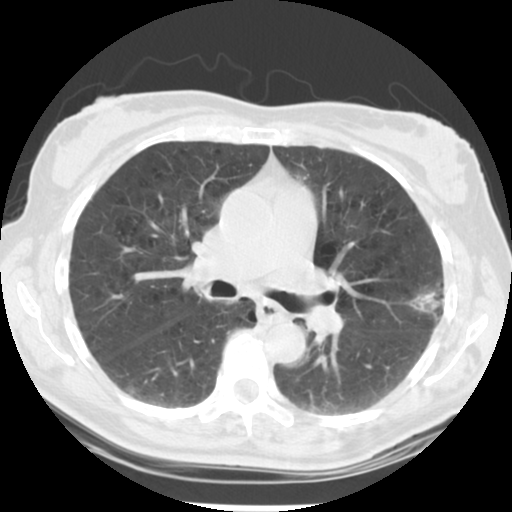
Low-dose screening chest CT, one axial slice. Slice 130 of 223 in the series (ordered by position). Reconstruction kernel STANDARD. Lung window (W 1500 / L -600 HU). 2.5 mm slice thickness. 512 × 512 image matrix.
Structures marked on this image (manually delineated by an expert):
- lesion 1 (tumor, upper lobe of left lung): box from (x=410, y=281) to (x=444, y=322) px